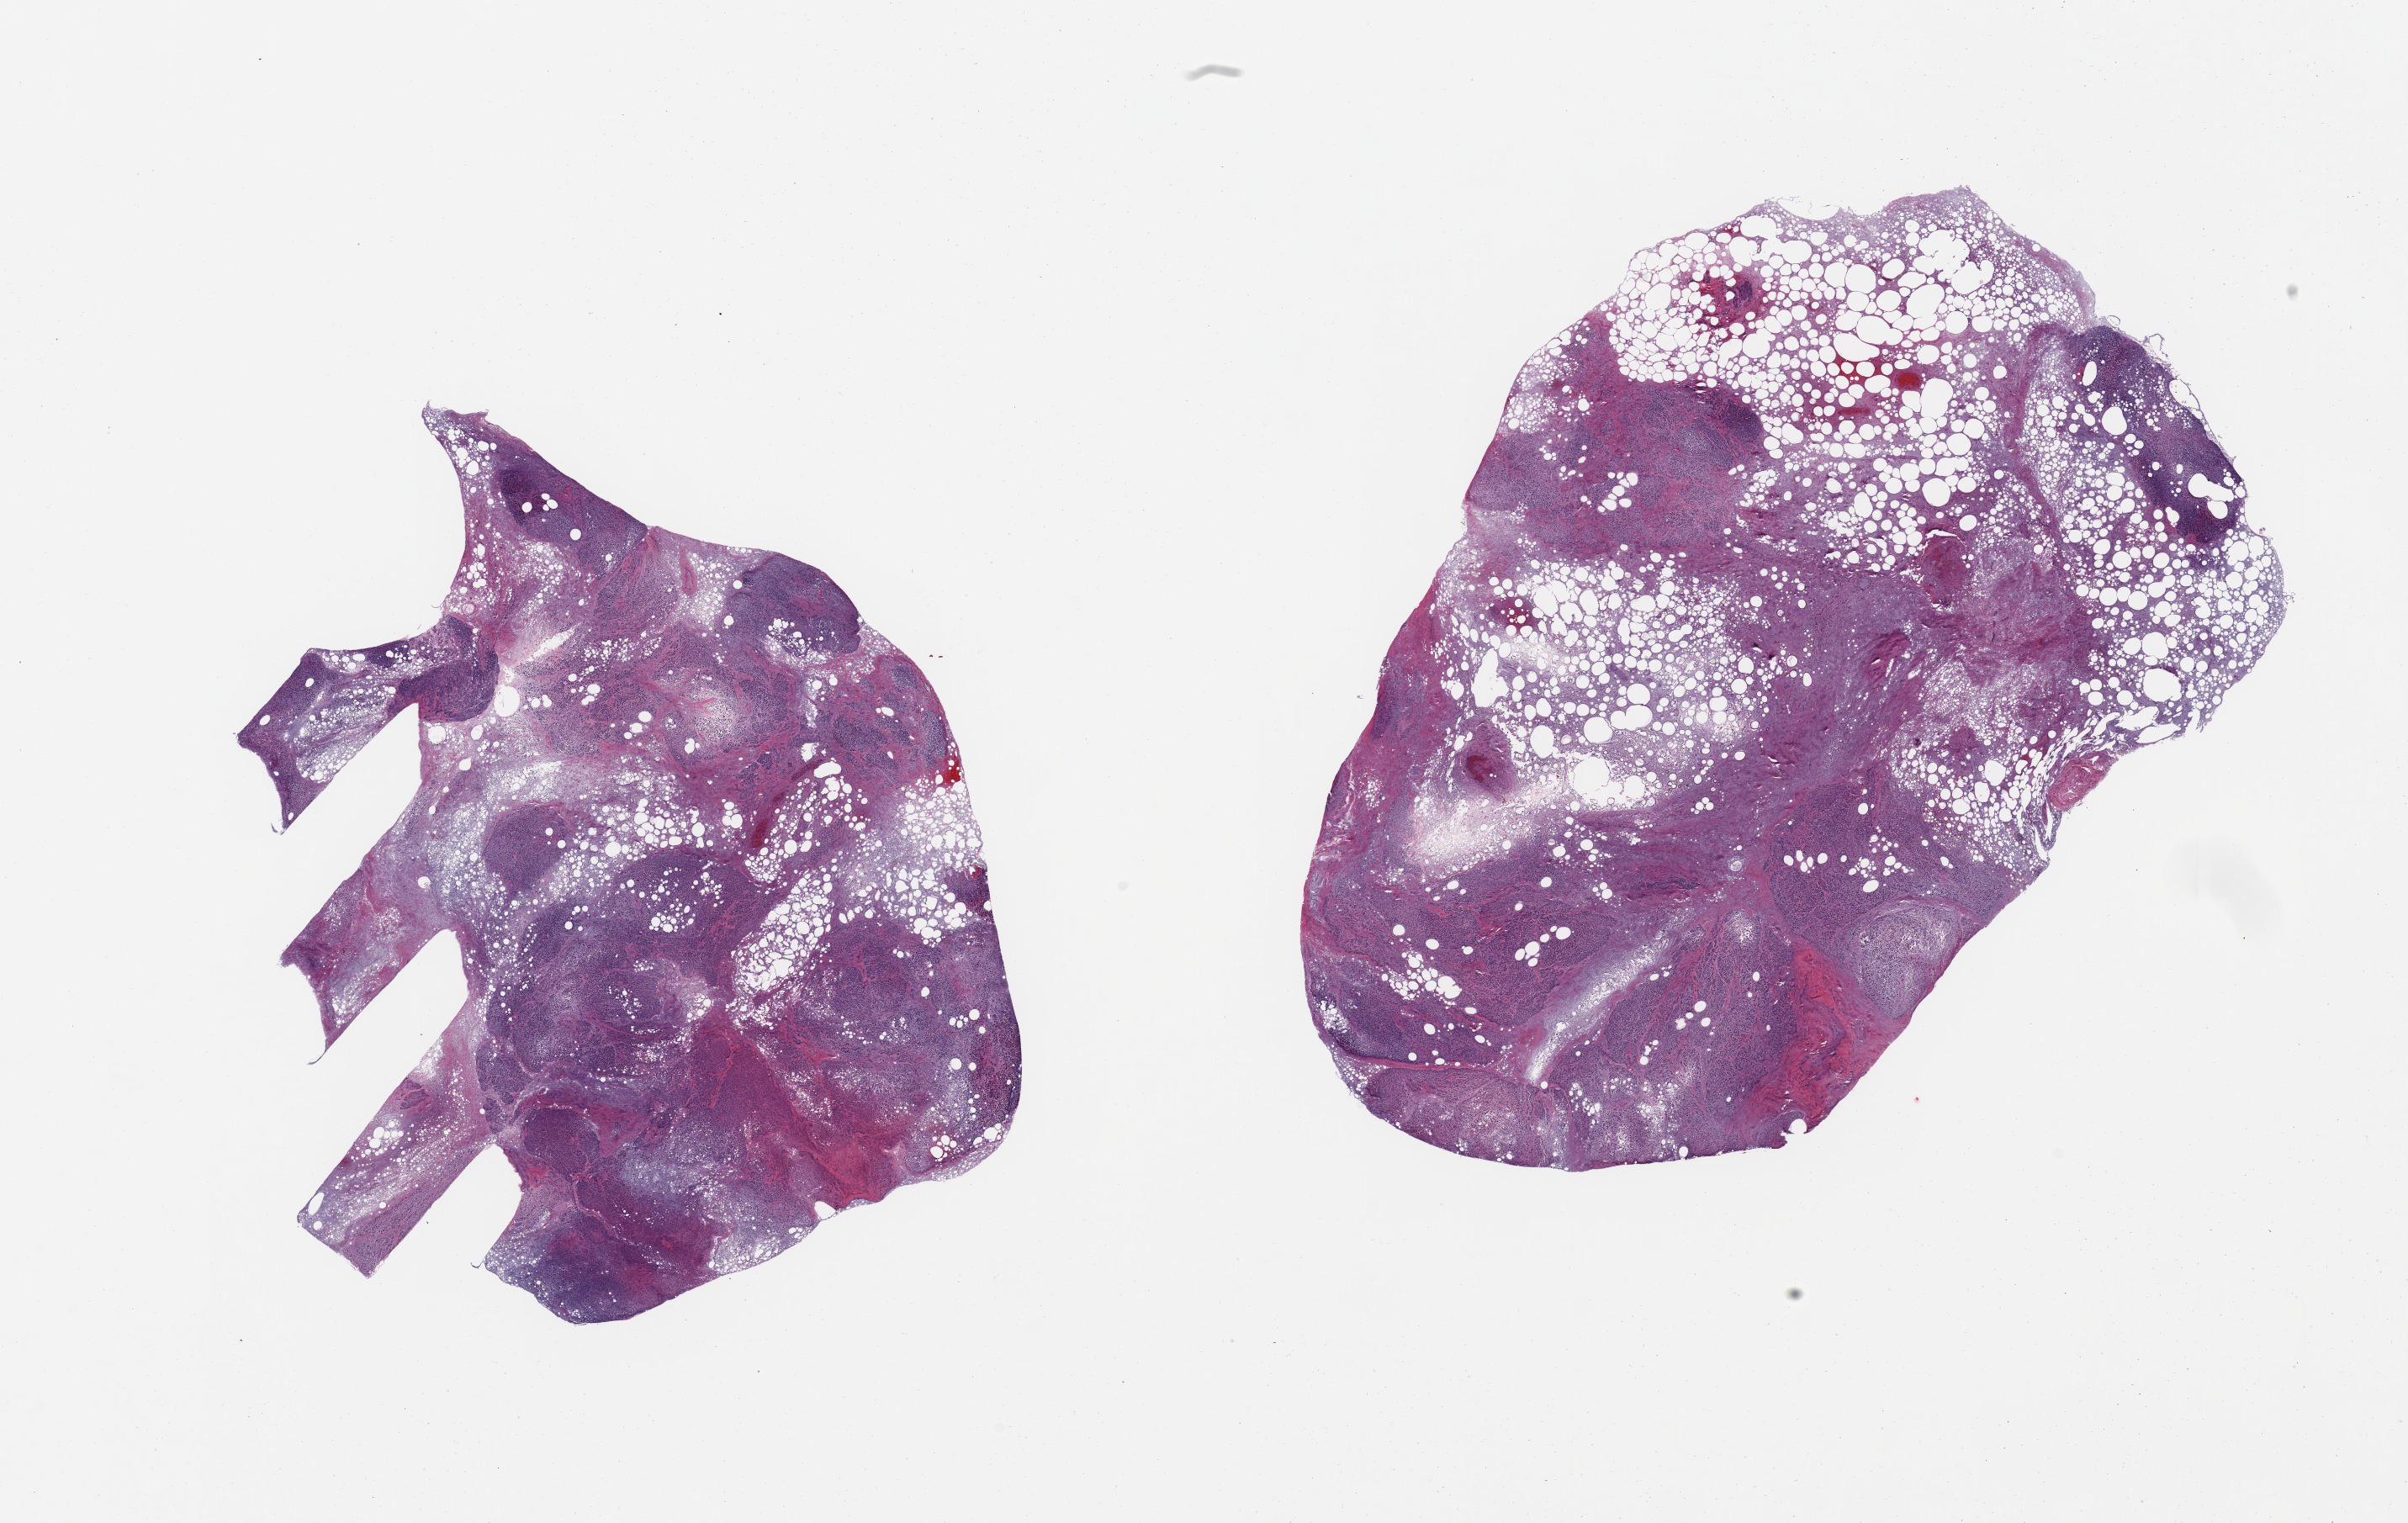
Digitized haematoxylin and eosin-stained section, whole scanned area (about 22.6 x 14.3 mm) shown as a low-resolution overview. PAXgene-fixed, paraffin-embedded tissue. Target tissue: pancreas. Tissue donor sample. Female donor.
Reviewer comment on this tissue sample: 2 pieces, advanced saponification. Islets not visible.